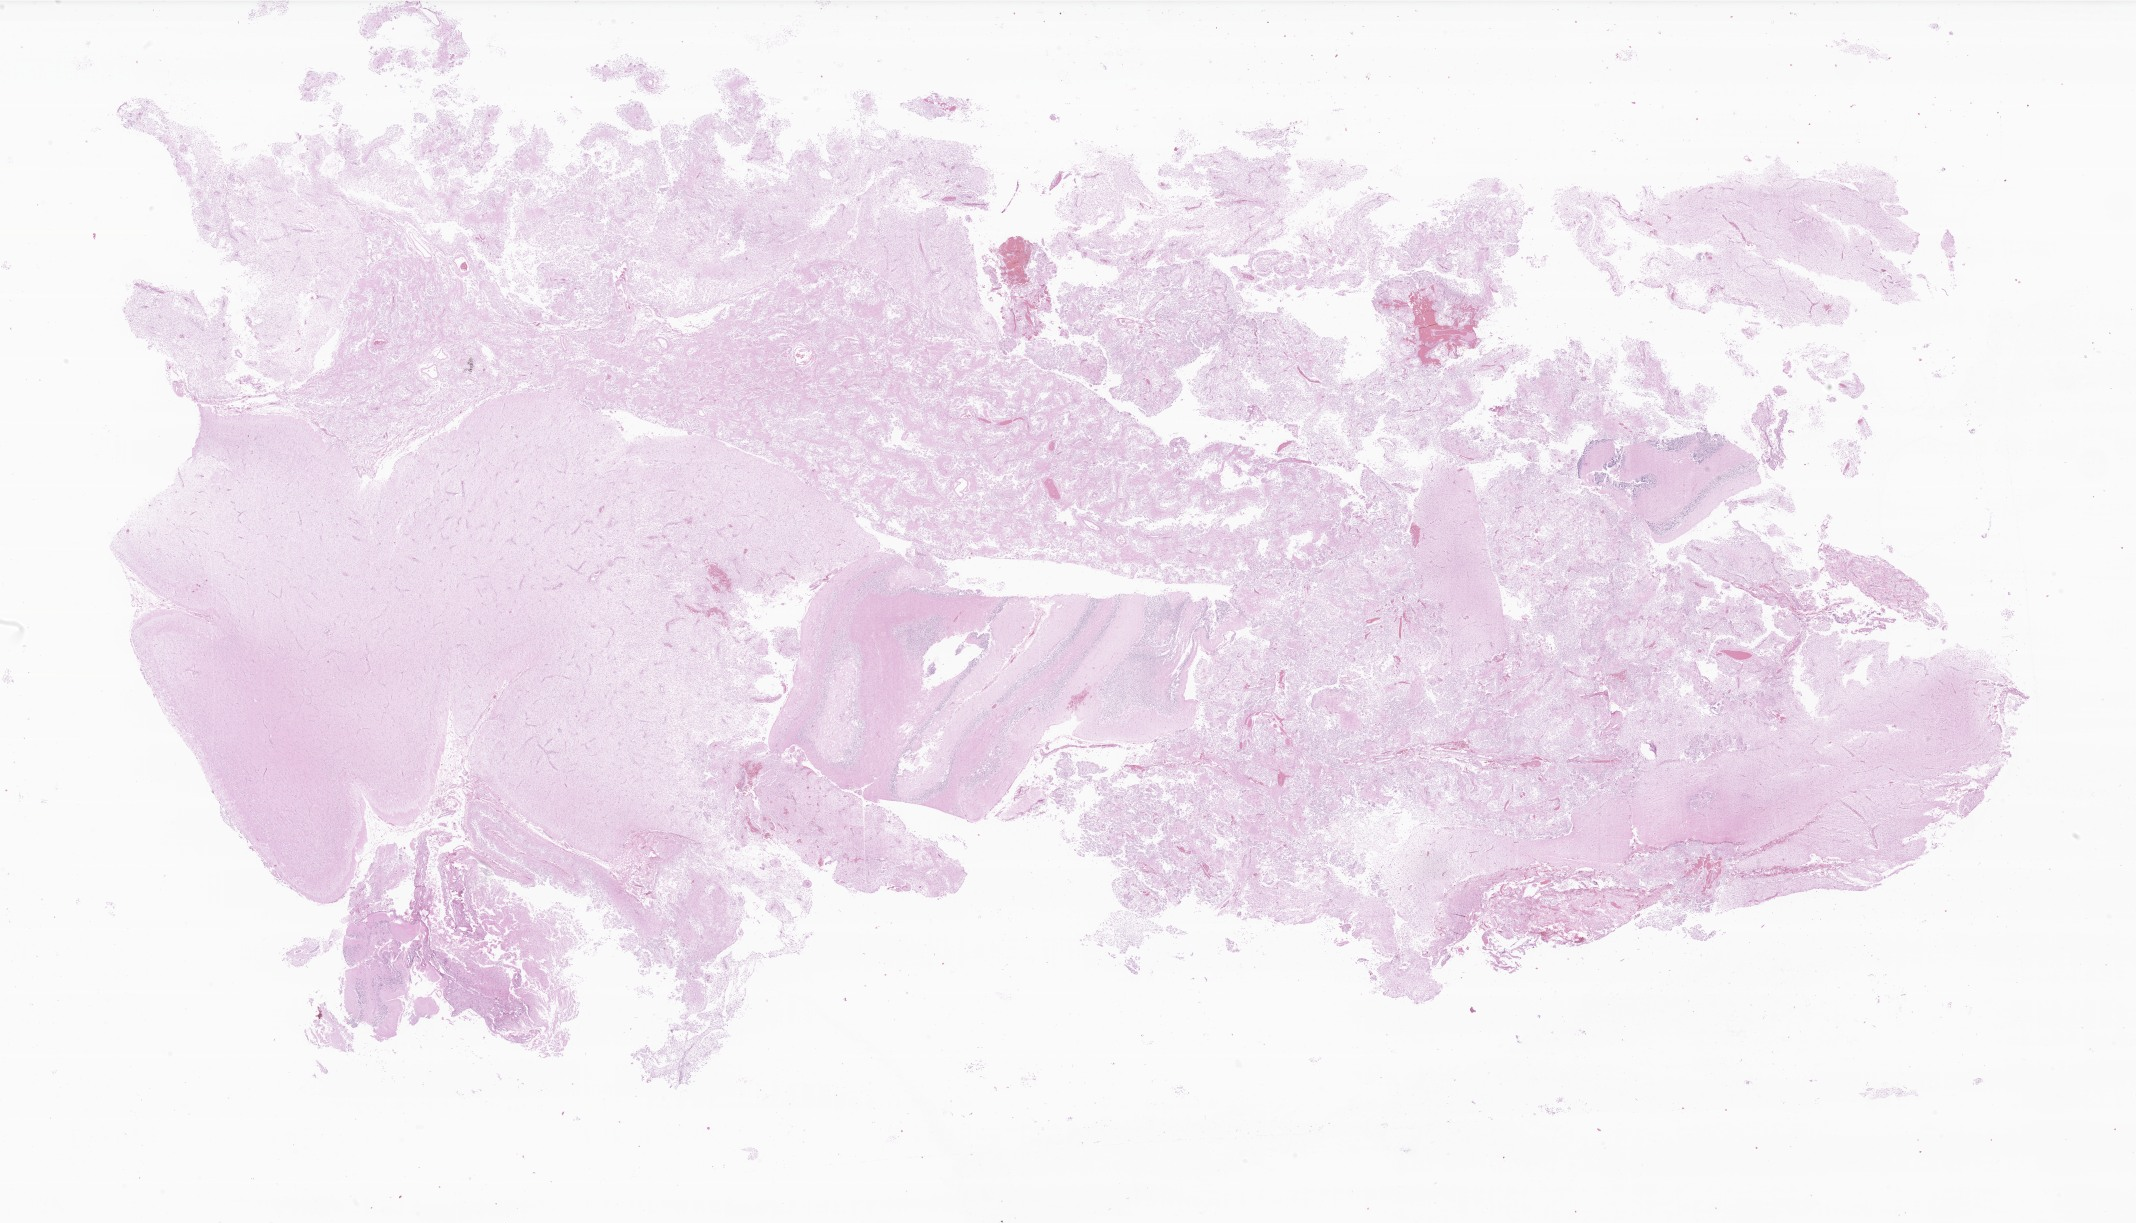
Digitized hematoxylin and eosin (H&E)-stained section of tumor tissue from the brain, a low-resolution overview of the entire scanned area, about 36.0 x 20.6 mm, formalin-fixed paraffin-embedded section. Female patient, age 34 months.
• recorded diagnosis: Pilocytic astrocytoma